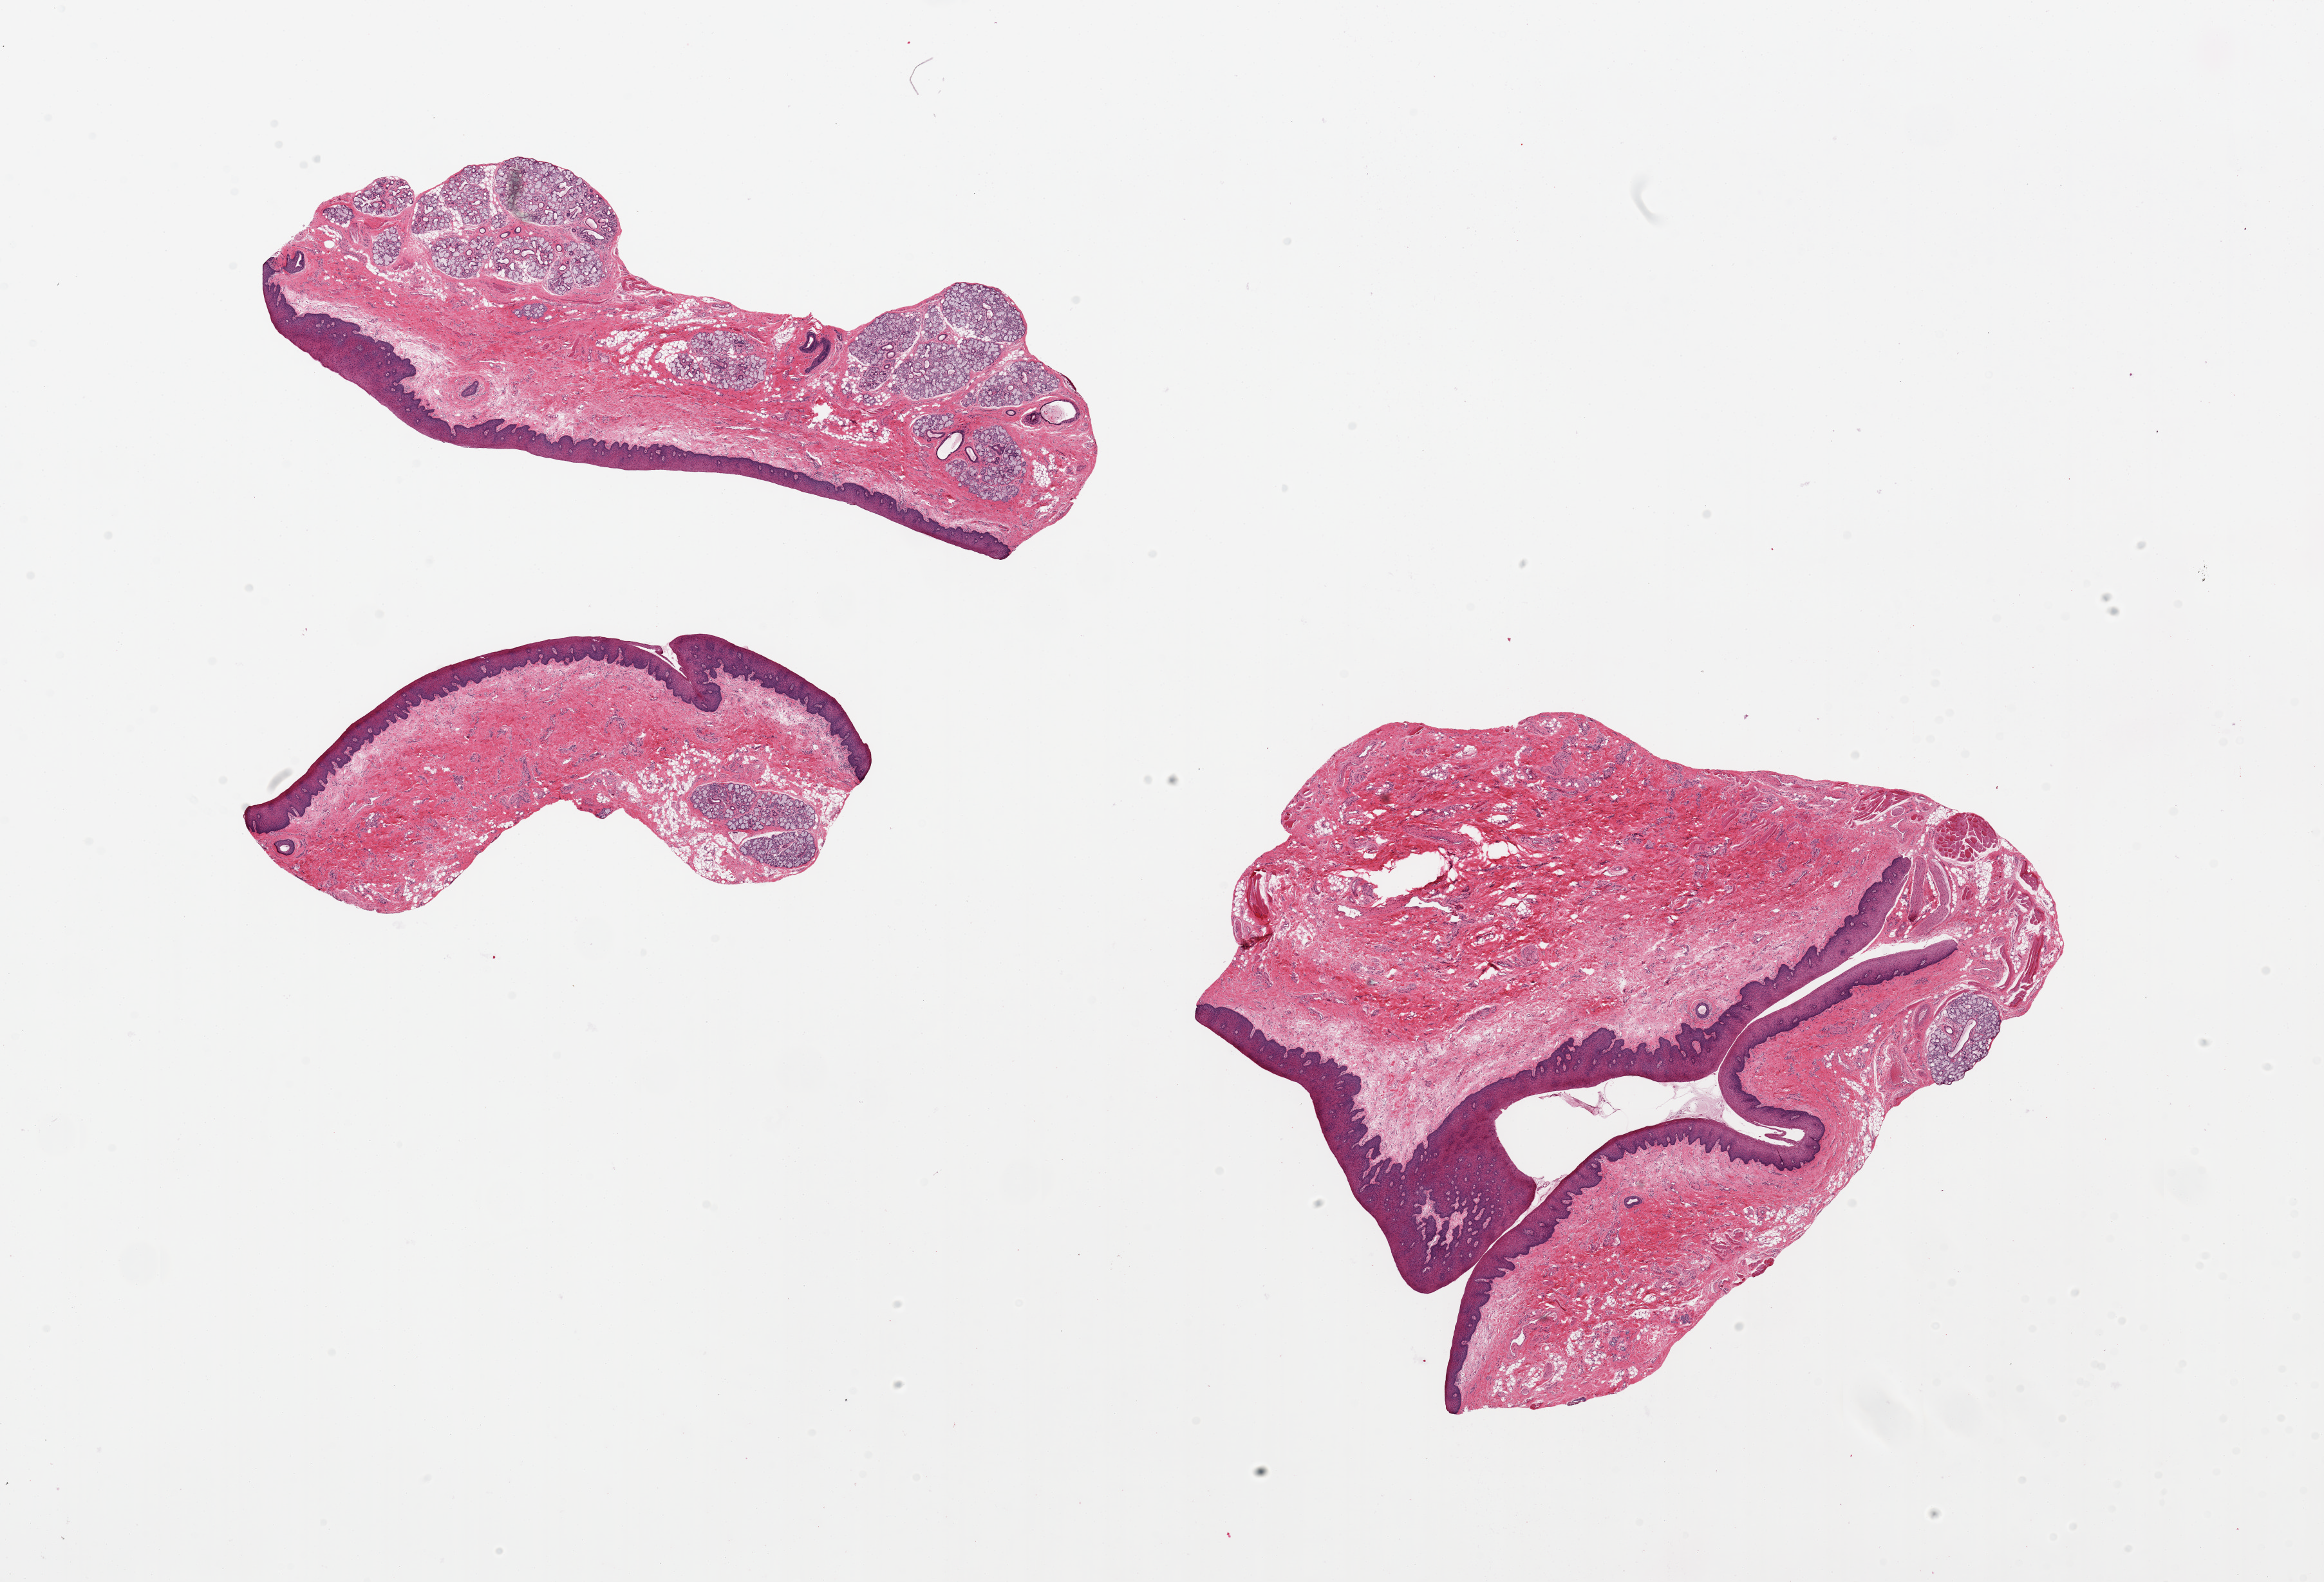
H&E whole-slide image — low-resolution overview of the scanned area, about 28.5 x 19.4 mm (from a 20x scan), PAXgene-fixed, paraffin-embedded tissue, section of minor salivary gland (target tissue), donor tissue sample. Donor sex: male.
Review note (as recorded): 3 pieces, from 7.5x2 to 9x8mm; glands are 5 to 50% in the 3 pieces; too much skin in sample.